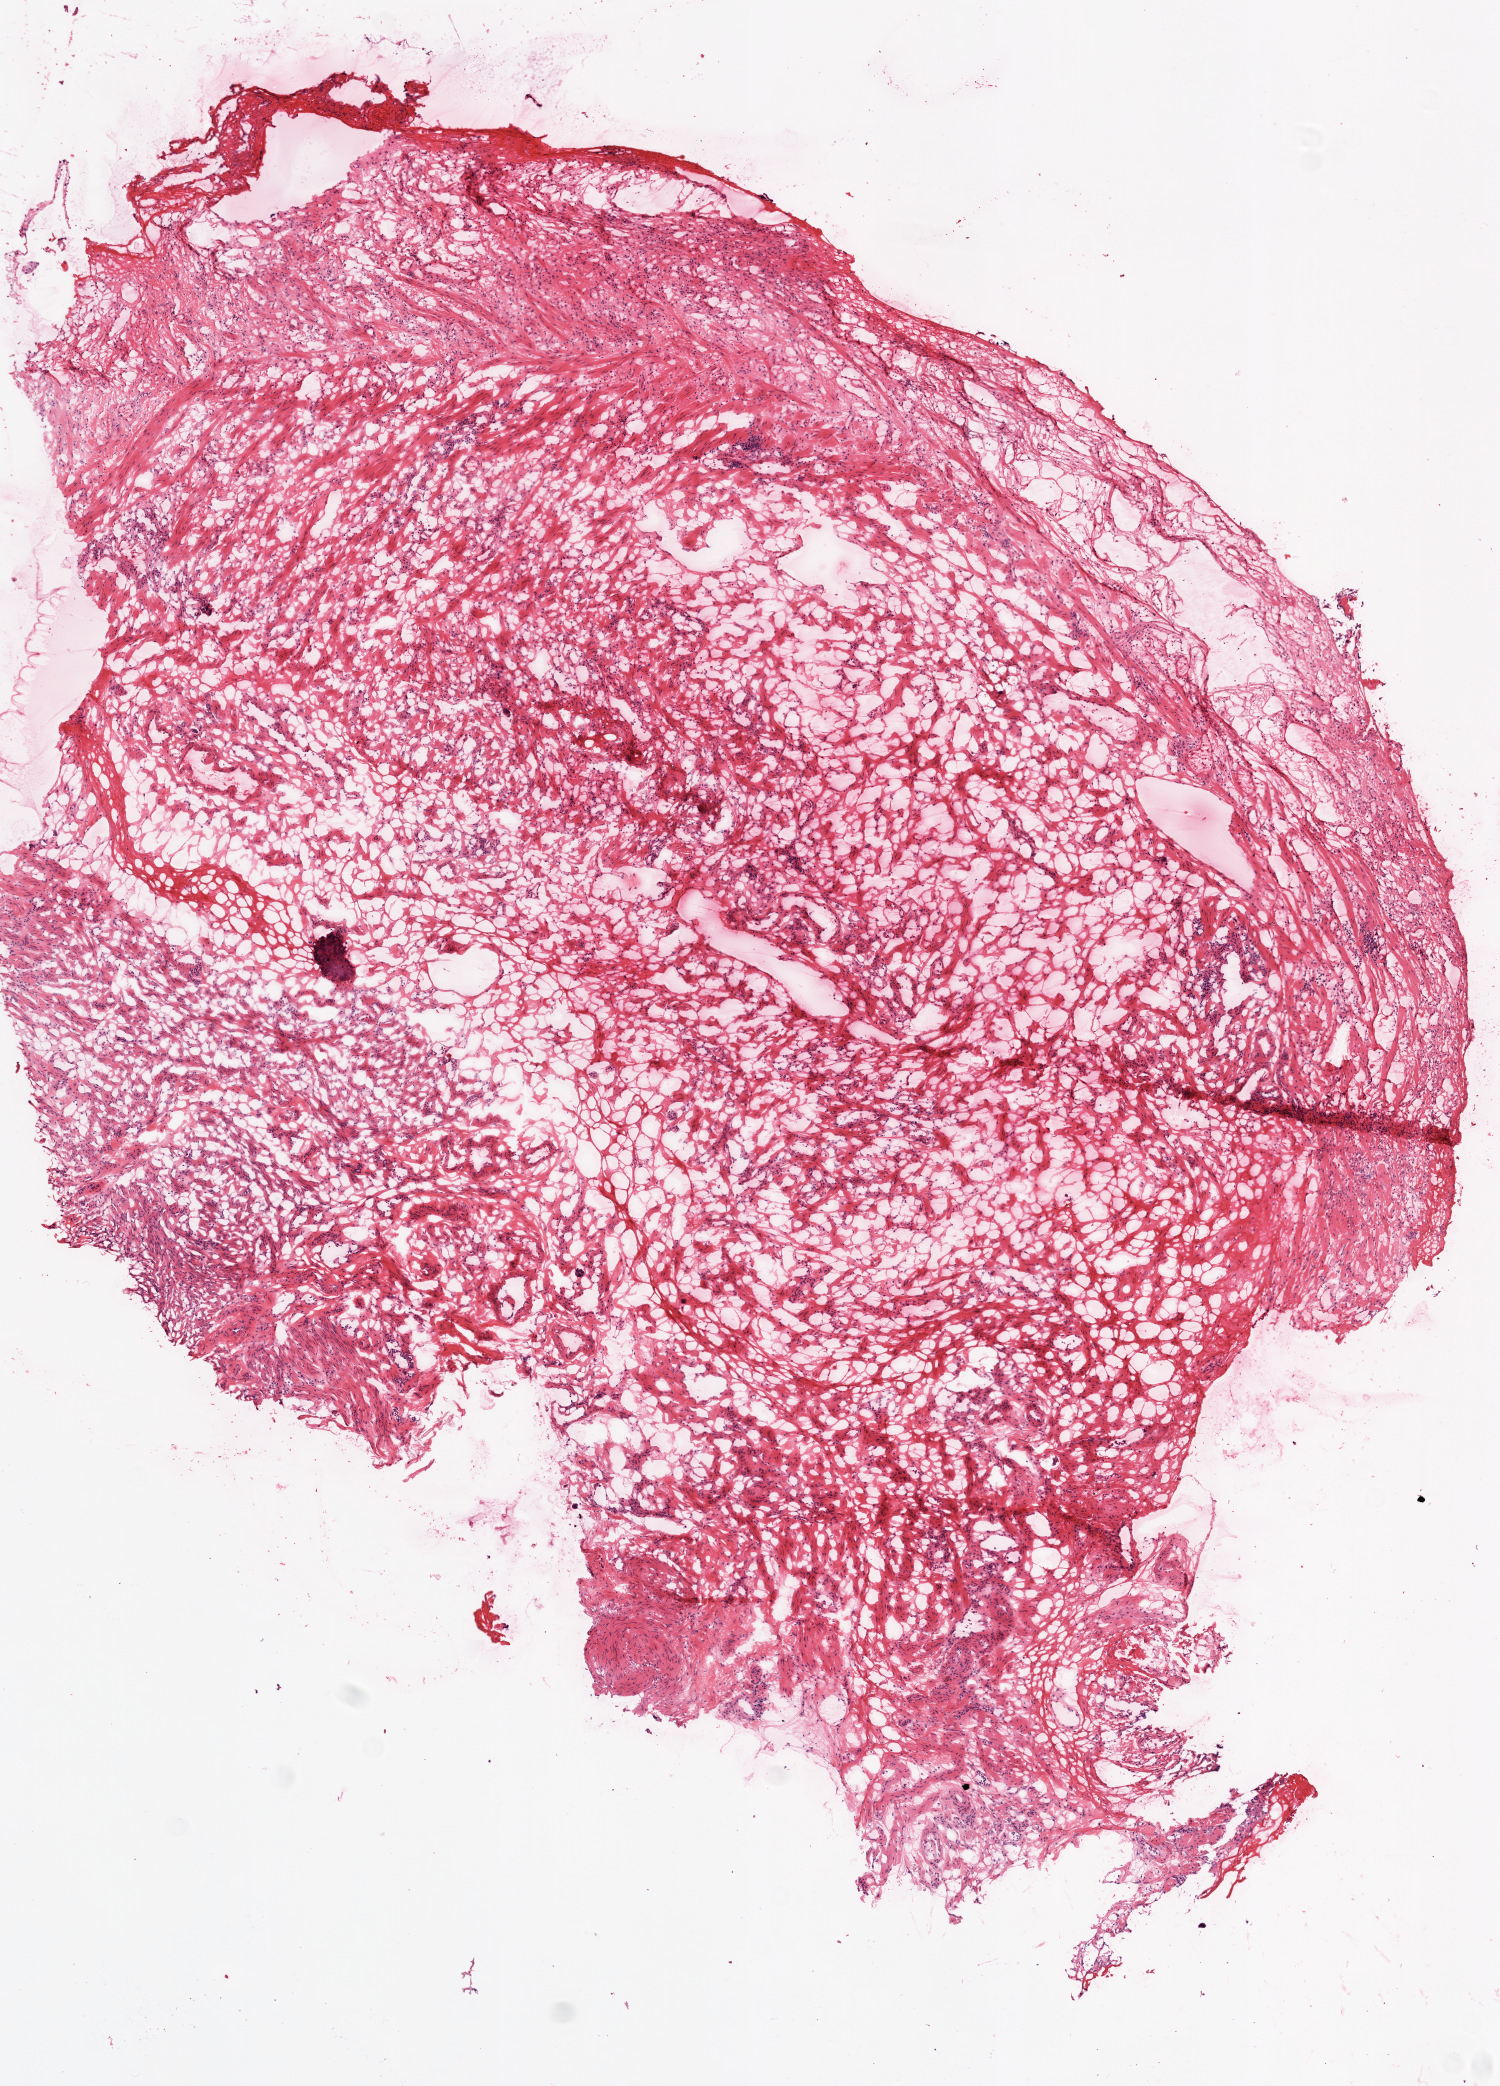
H&E whole-slide image — low-resolution overview of the scanned area, about 6.0 x 8.4 mm (acquisition: 20x scan), frozen section from the top of the tissue portion, sample: solid tissue normal (non-tumour tissue), ovary. Female, age 53 years at initial diagnosis.
This section: solid tissue normal (non-tumour) sample from the same patient. Patient diagnosis: Serous surface papillary carcinoma.